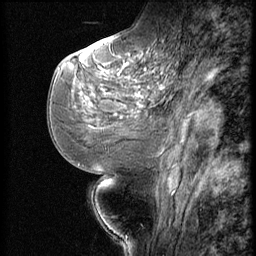
Breast MRI (dynamic contrast-enhanced), one sagittal slice; slice 25 of 56 in the series (ordered by position); dynamic contrast-enhanced series, image 2 of 3 at this slice position (ordered by acquisition); 1.5 T; TE 4.2 ms, TR 9 ms; 2.5 mm slice thickness; 256 × 256 image matrix, field of view 180 × 180 mm. Patient: female, 51 years. From the clinical record (not read from this slice): setting: breast cancer imaged before/during neoadjuvant chemotherapy; receptor status: triple-negative.
Annotated regions visible in this slice (semi-automatically segmented with operator editing):
- analysis volume of interest (the breast-tissue region the enhancement analysis was run in; not a lesion): bounding box [x1, y1, x2, y2] px = [73, 46, 172, 147]
- tumour enhancement mask (voxels above the 140 % enhancement threshold inside the analysis volume of interest): [108, 64, 129, 73]